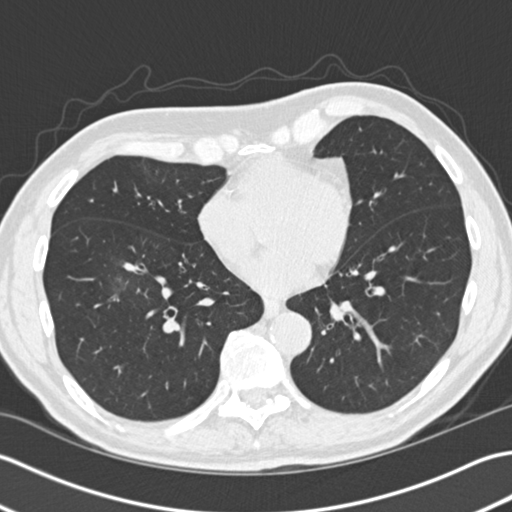
Low-dose screening chest CT, one axial slice; position 65 of 172 along the scan axis; reconstruction kernel B30f; 120 kVp; lung window (W 1500 / L -600 HU); 2 mm slice thickness; 512 × 512 image matrix.
Annotated regions visible in this slice (manually delineated by an expert):
- lesion 1 (tumor, lower lobe of right lung): box from (x=123, y=262) to (x=145, y=273) px